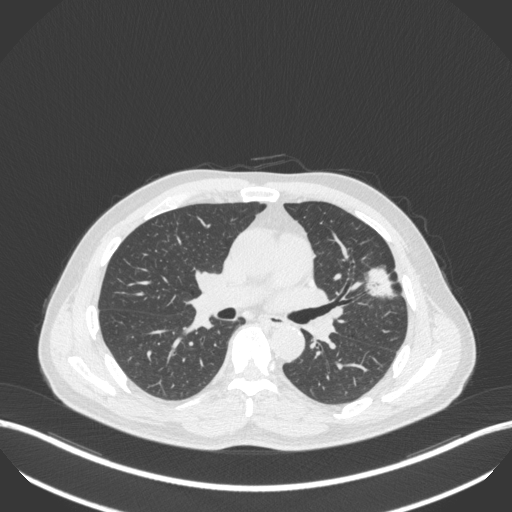
Chest CT, one axial slice; 120 kVp; lung window (W 1500 / L -600 HU); 512 × 512 image matrix, field of view 400 × 400 mm. Patient: male, 55 years. From the clinical record (not read from this slice): clinical TNM (as recorded): T1c N0 M0.
Structures marked on this image (bounding box drawn by a radiologist):
- lung tumour (recorded histology: adenocarcinoma): bounding box [x1, y1, x2, y2] px = [362, 264, 401, 301]